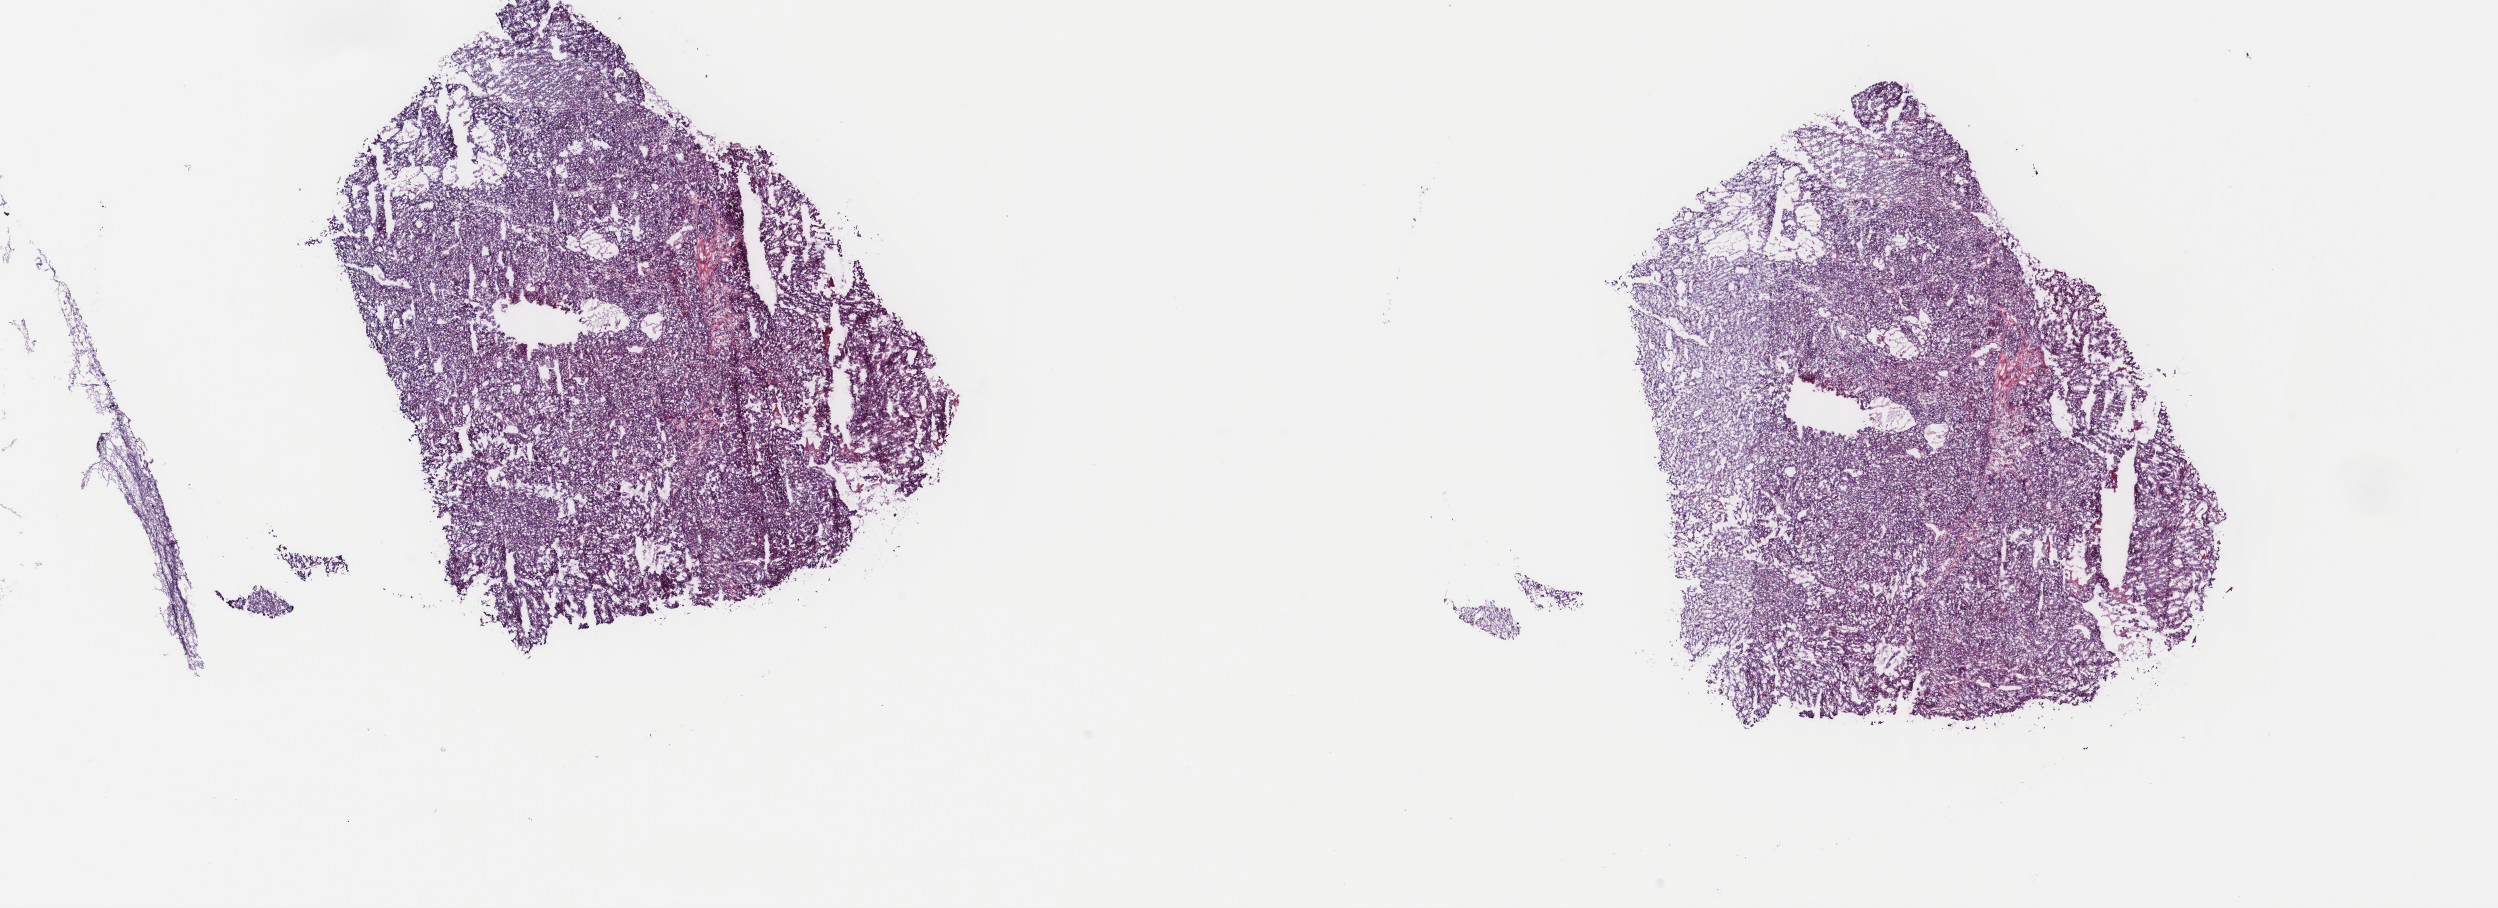
H&E whole-slide image — shown as a low-resolution overview of the whole scanned area (about 19.8 x 7.2 mm, acquisition: 40x scan). Frozen section. Primary tumour sample from the liver. Male patient; age at initial diagnosis 24 years. Histologic grade: G3 (poorly differentiated). Pathologist review of this section (percent, as recorded): tumour cells 90%, tumour nuclei 90%, normal cells 0%, stromal cells 10%, necrosis 0%. Infiltration values recorded for this section: lymphocyte infiltration 0%, monocyte infiltration 0%, neutrophil infiltration 0%.
• AJCC pathologic stage: II (6th edition)
• diagnosis: Hepatocellular carcinoma, NOS